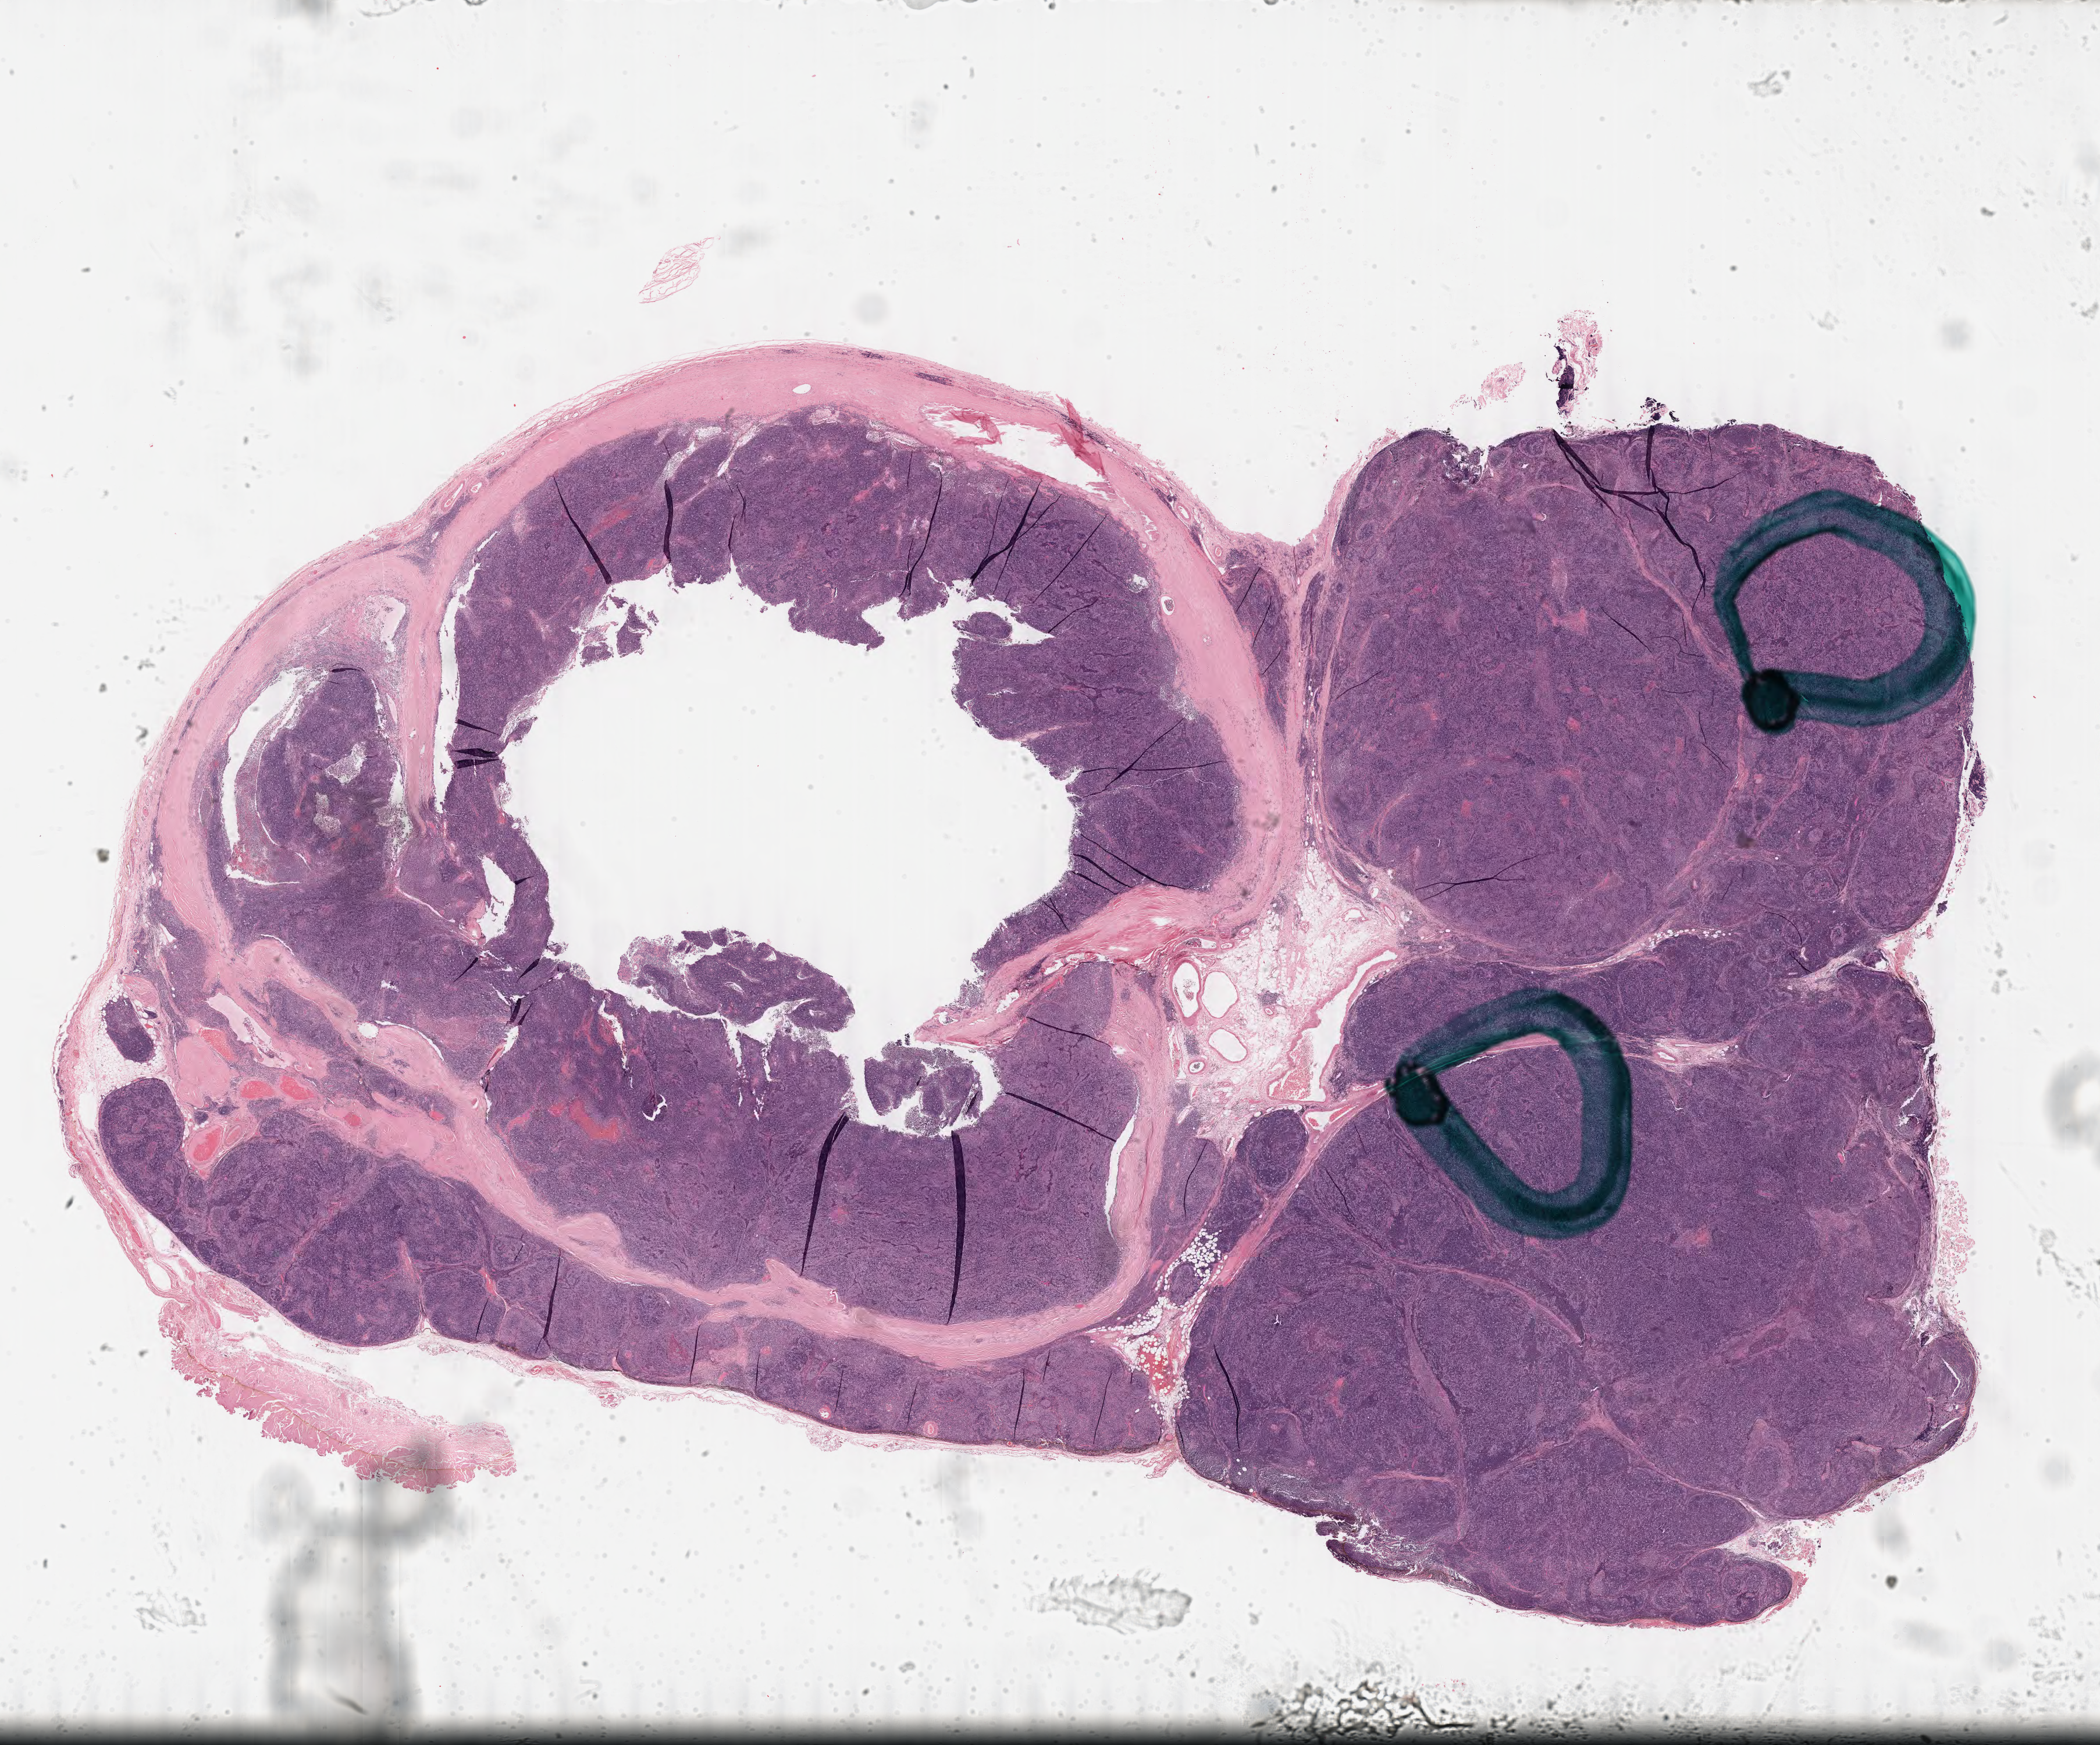
Whole-slide histology image, H&E-stained — low-resolution overview of the scanned area, about 28.5 x 23.7 mm (slide scanned at 40x). Formalin-fixed paraffin-embedded (FFPE) diagnostic section. Sample: primary tumour, thymus. Female, age 44 years at initial diagnosis.
Diagnosis: Thymoma, type B2, malignant.